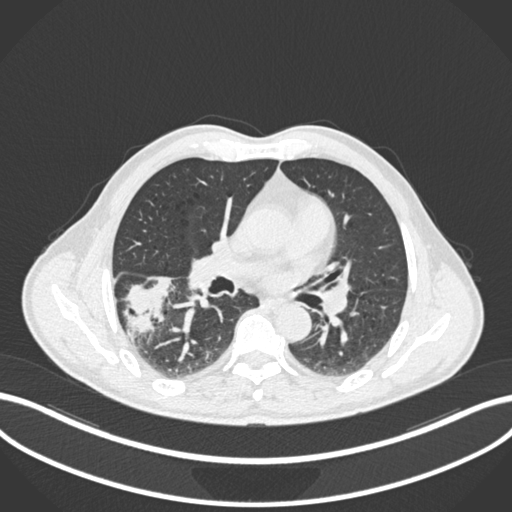
Chest CT, one axial slice. Slice 105 of 208 in the series (ordered by position). Reconstruction kernel B30f. Lung window (W 1500 / L -600 HU). 512 × 512 image matrix, field of view 400 × 400 mm. Male patient, age 58 years. Case-level facts recorded for this patient, not image findings: clinical TNM (as recorded): T3 N0 M0.
Outlined on this slice (rectangle marked by the reading radiologist):
- lung tumour (recorded histology: squamous cell carcinoma): bounding box <121,266,176,339> (left, top, right, bottom; pixels)